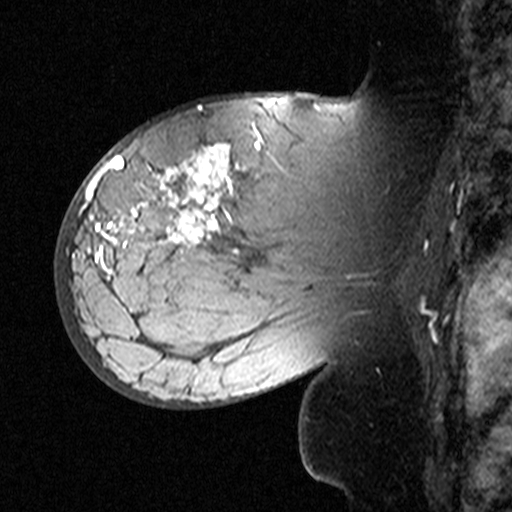
Breast MRI (dynamic contrast-enhanced), one sagittal slice. Position 28 of 44 along the scan axis. Dynamic contrast-enhanced study with each time point stored as its own series, time point 2 of 3 at this slice position (early post-contrast, ordered by acquisition time). 1.5 T. TE 4.5 ms, TR 11 ms. 3 mm slice thickness. 512 × 512 image matrix, field of view 200 × 200 mm. Female patient, age 53 years. Case-level facts recorded for this patient, not image findings: setting: breast cancer imaged before/during neoadjuvant chemotherapy; receptor status: HR-positive, HER2-negative.
Structures marked on this image (semi-automatically segmented with operator editing):
- analysis volume of interest (the breast-tissue region the enhancement analysis was run in; not a lesion): bounding box (x1, y1, x2, y2) in pixels: (76, 140, 311, 353)
- tumour enhancement mask (voxels above the 90 % enhancement threshold inside the analysis volume of interest): (99, 143, 261, 280)